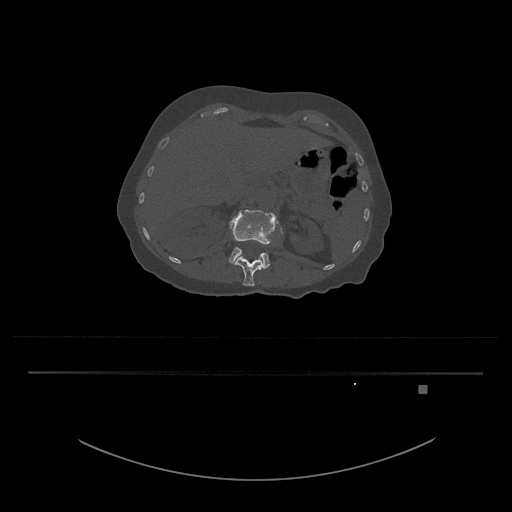
CT including the spine, one axial slice. Position 525 of 797 along the scan axis. Reconstruction kernel Br40s/3. 120 kVp. Bone window (W 1800 / L 400 HU). 512 × 512 image matrix, field of view 500 × 500 mm. Patient: female, 57 years. Case-level facts recorded for this patient, not image findings: primary cancer: cervical.
Structures marked on this image (semi-automatically segmented with operator editing):
- L1 vertebra: bounding box <234,228,283,286> (left, top, right, bottom; pixels)